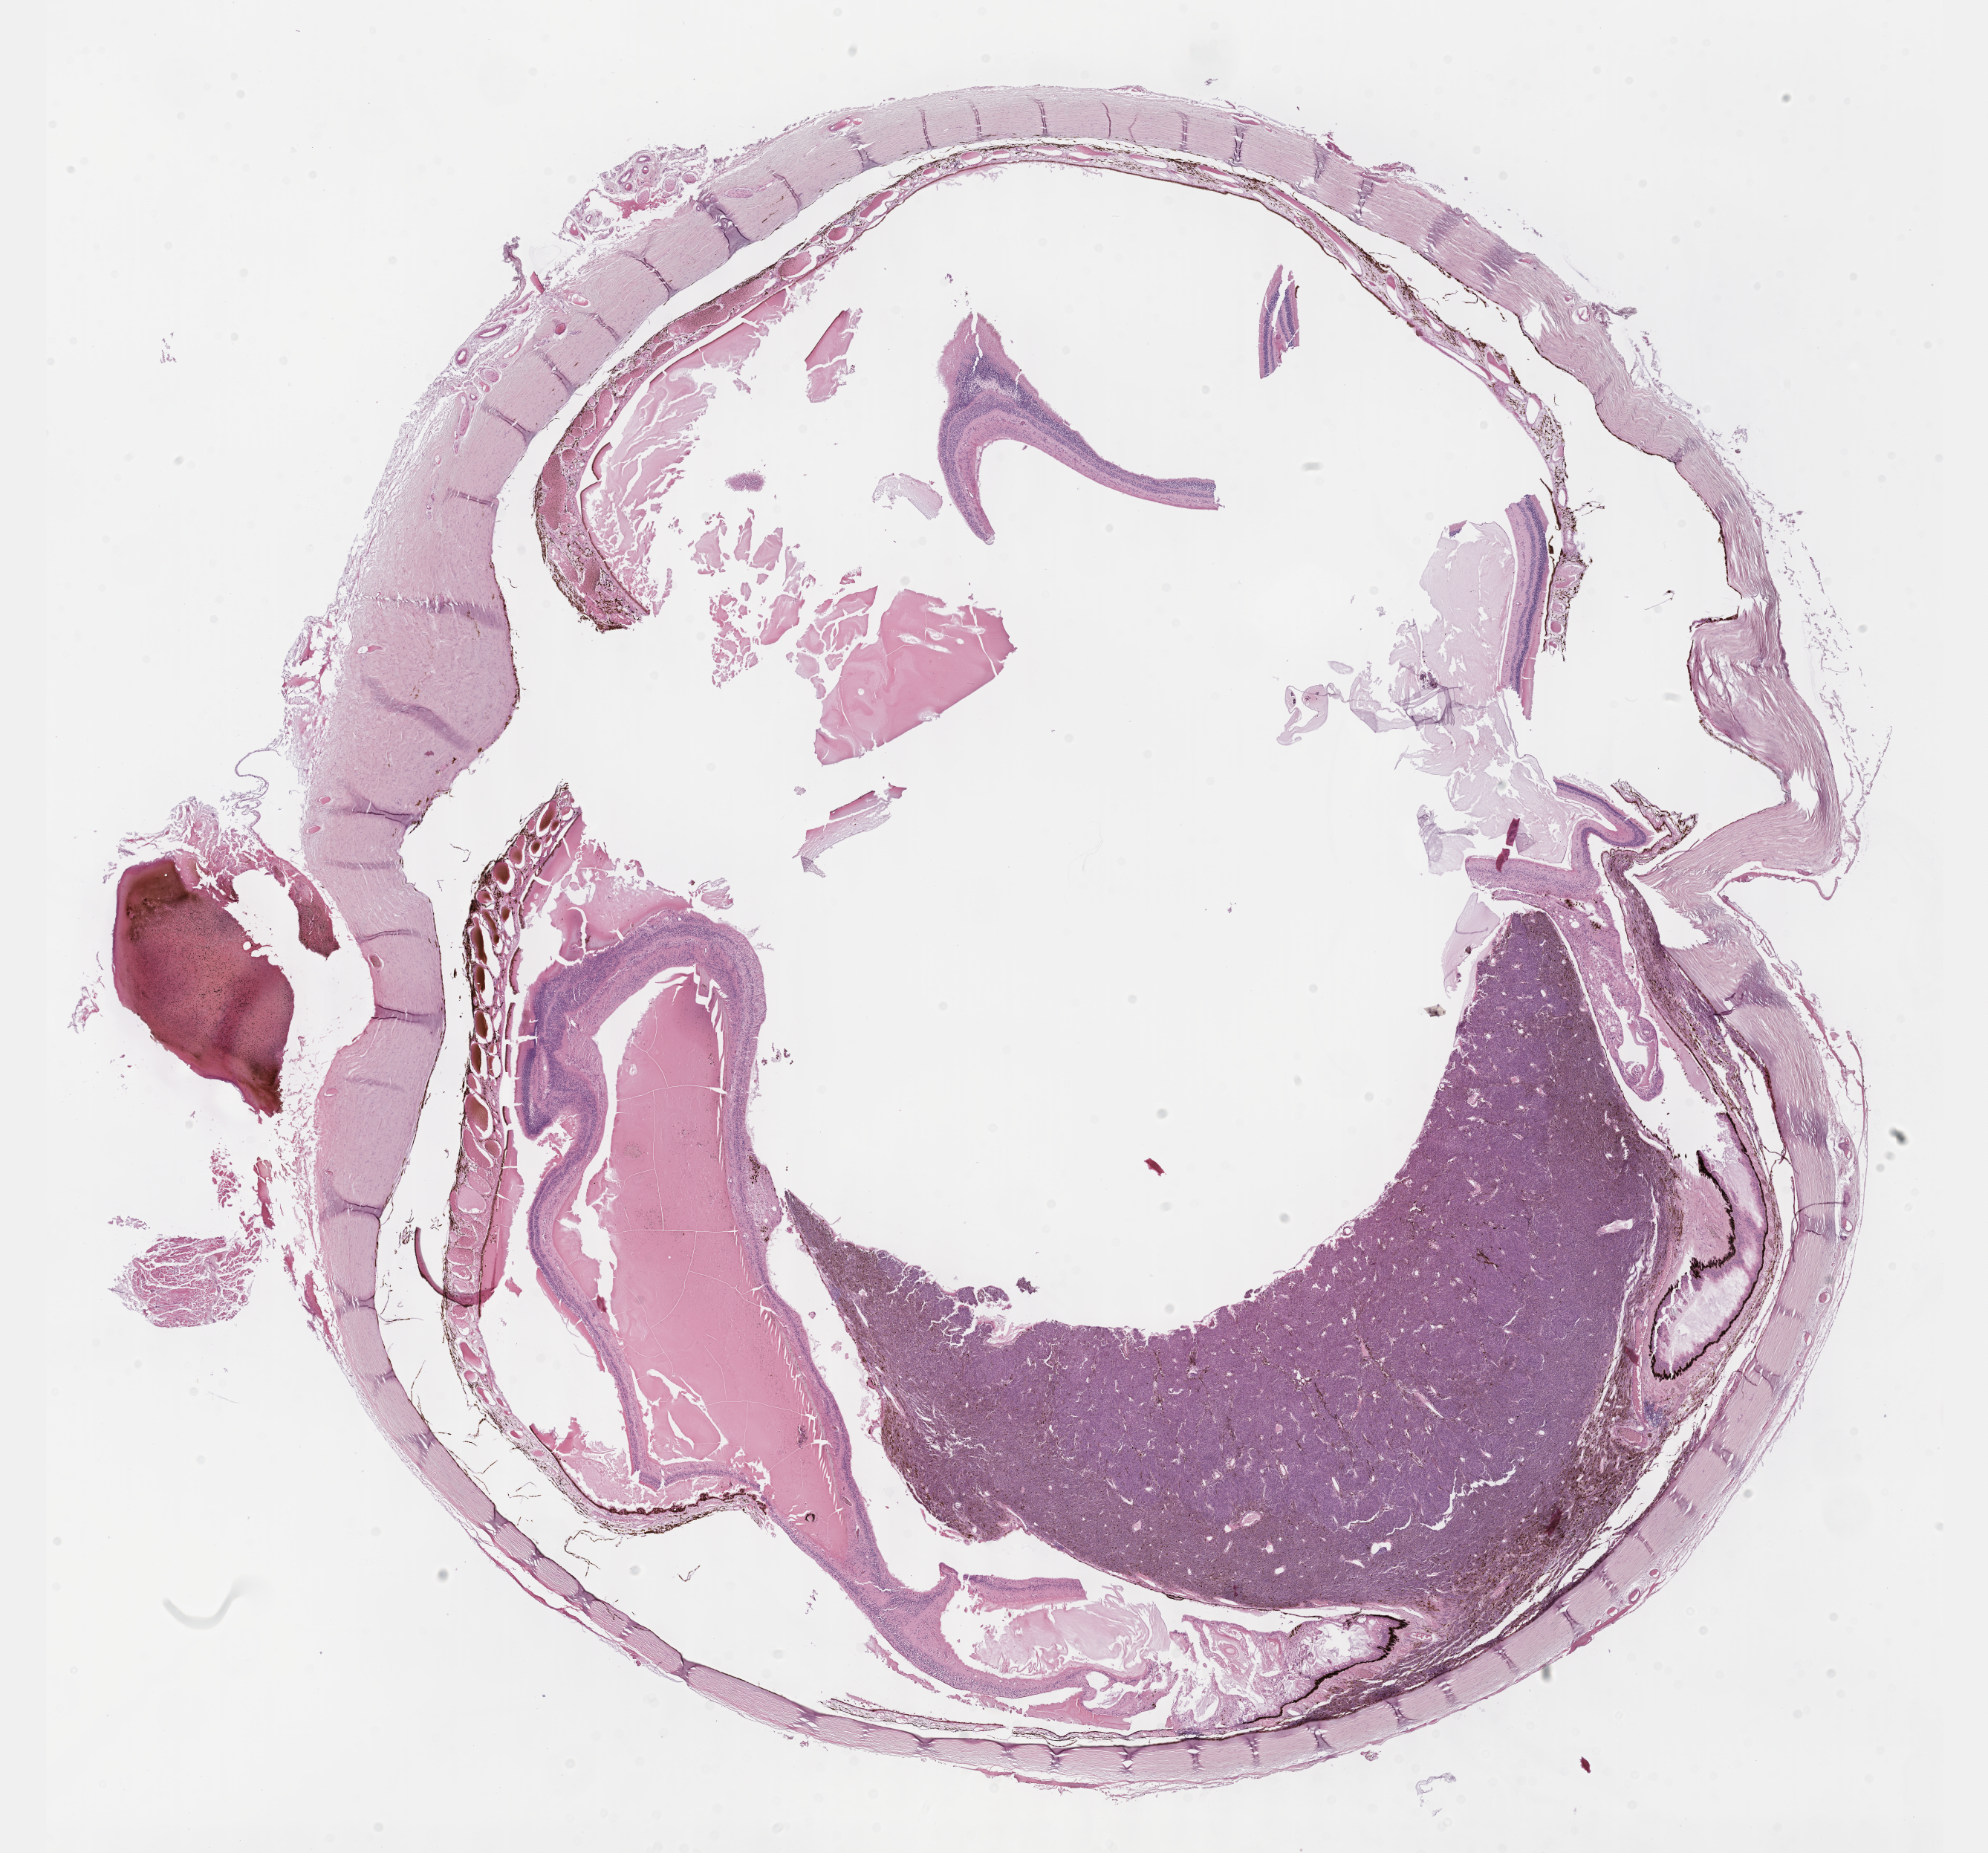
Whole-slide histology image, Hematoxylin and eosin (H&E) stained, a low-resolution overview of the entire scanned area, about 21.6 x 20.2 mm, formalin-fixed paraffin-embedded (FFPE) diagnostic section, uvea, primary tumour sample. Male patient; age at initial diagnosis 53 years.
Histologic diagnosis: Spindle cell melanoma, NOS (choroid).